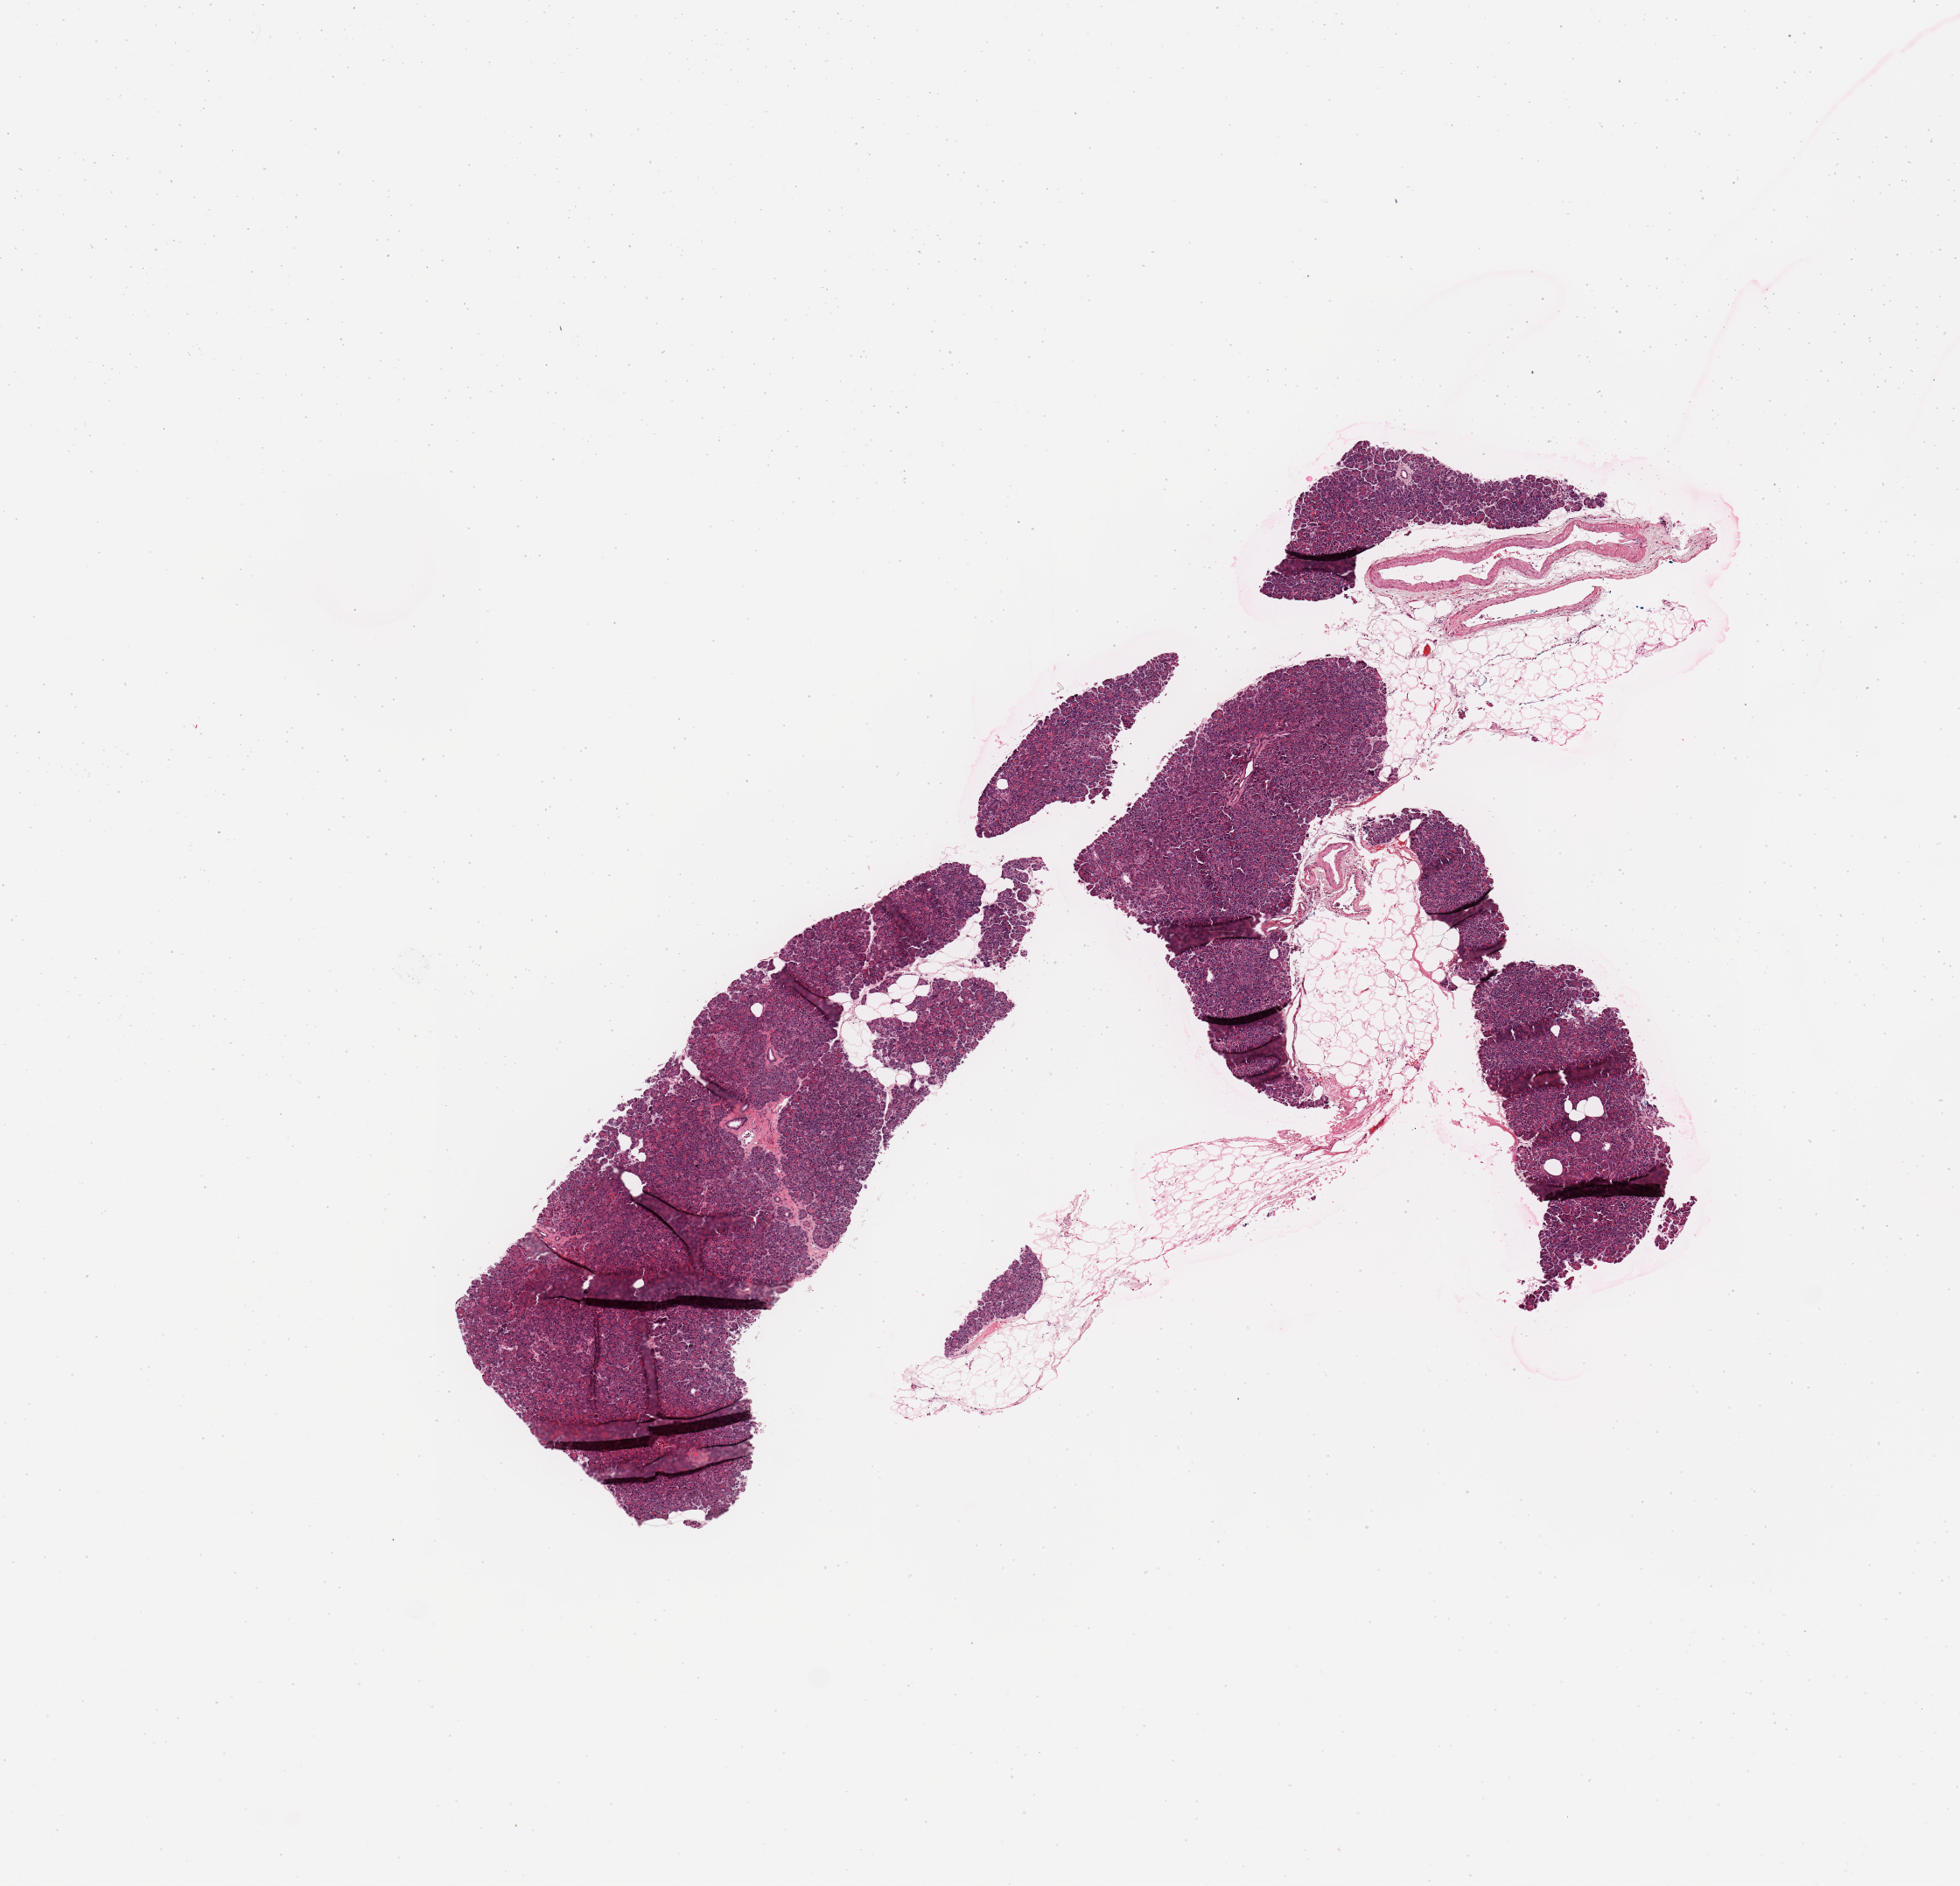
Hematoxylin and eosin (H&E) stained whole-slide image, low-resolution overview of the scanned area, about 8.9 x 8.5 mm. Normal (non-tumour) tissue sample, sampled site: pancreas. Female, 58 y/o.
This section: normal (non-tumour) tissue from the same patient. Patient diagnosis: Infiltrating duct carcinoma, NOS.